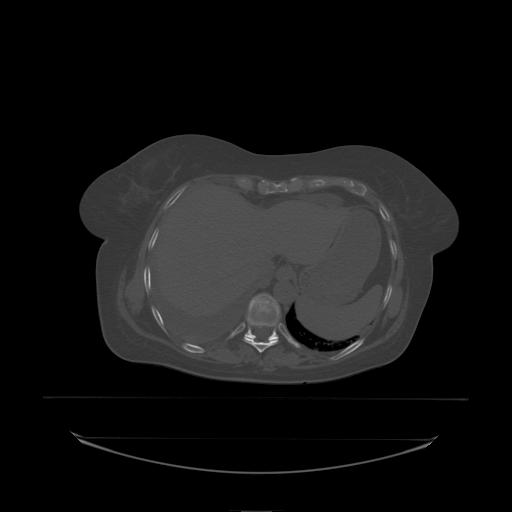
CT including the spine, one axial slice. Position 120 of 242 along the scan axis. Bone window (W 1800 / L 400 HU). 2.5 mm slice thickness. 512 × 512 image matrix, field of view 500 × 500 mm. Patient: female, 53 years. Case-level facts recorded for this patient, not image findings: primary cancer: lung; vertebrae with lytic lesions (as recorded): T7, L1.
Annotated regions visible in this slice (semi-automatically segmented with operator editing):
- T10 vertebra: box from (x=245, y=294) to (x=280, y=338) px
- T9 vertebra: (x=248, y=315)–(x=277, y=326)